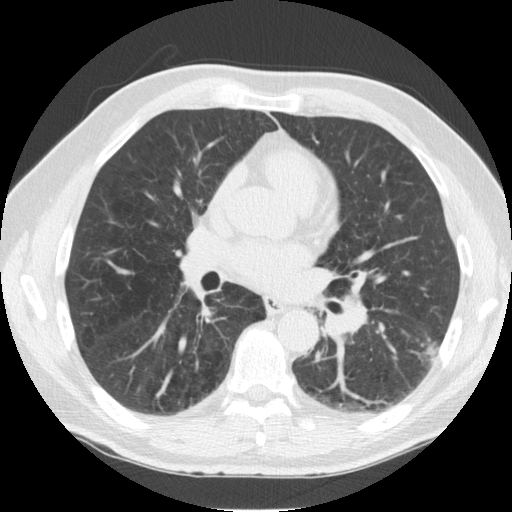
Axial slice from a low-dose chest CT screening exam; third screening round (two years after baseline); lung window (W 1500 / L -600 HU); slice 69 of 126 in the series; 512 × 512 image matrix, field of view 344 × 344 mm. Male, age 57 years at enrolment.
Lesion marked by an expert reader, bounding box [x1, y1, x2, y2] px = [406, 324, 449, 373]. Screening reader's record for this exam (one nodule recorded; not confirmed to be the boxed lesion): non-calcified nodule or mass ≥4 mm, left lower lobe, 13 × 12 mm, spiculated (stellate) margins, soft tissue attenuation, pre-existing on the prior screen: yes; interval growth: yes. Lung cancer was diagnosed 49 days after this screen: non-small cell carcinoma, left lower lobe, stage IV (AJCC 6th edition), 13 mm at pathology.